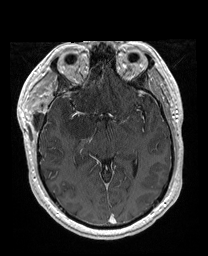
Brain MRI from a brain-tumour surgery series, one axial slice; position 105 of 176 along the scan axis; T1-weighted post-contrast; 1 mm slice thickness; 208 × 256 image matrix, field of view 208 × 256 mm. Case-level facts recorded for this patient, not image findings: histopathology: Astrocytoma; WHO grade: 4; IDH mutation: yes; tumour location: Right Orbitofrontal Anterior Temporal Insular.
Outlined on this slice (expert manual segmentation):
- previous resection cavity: bounding box [x1, y1, x2, y2] px = [85, 58, 99, 78]